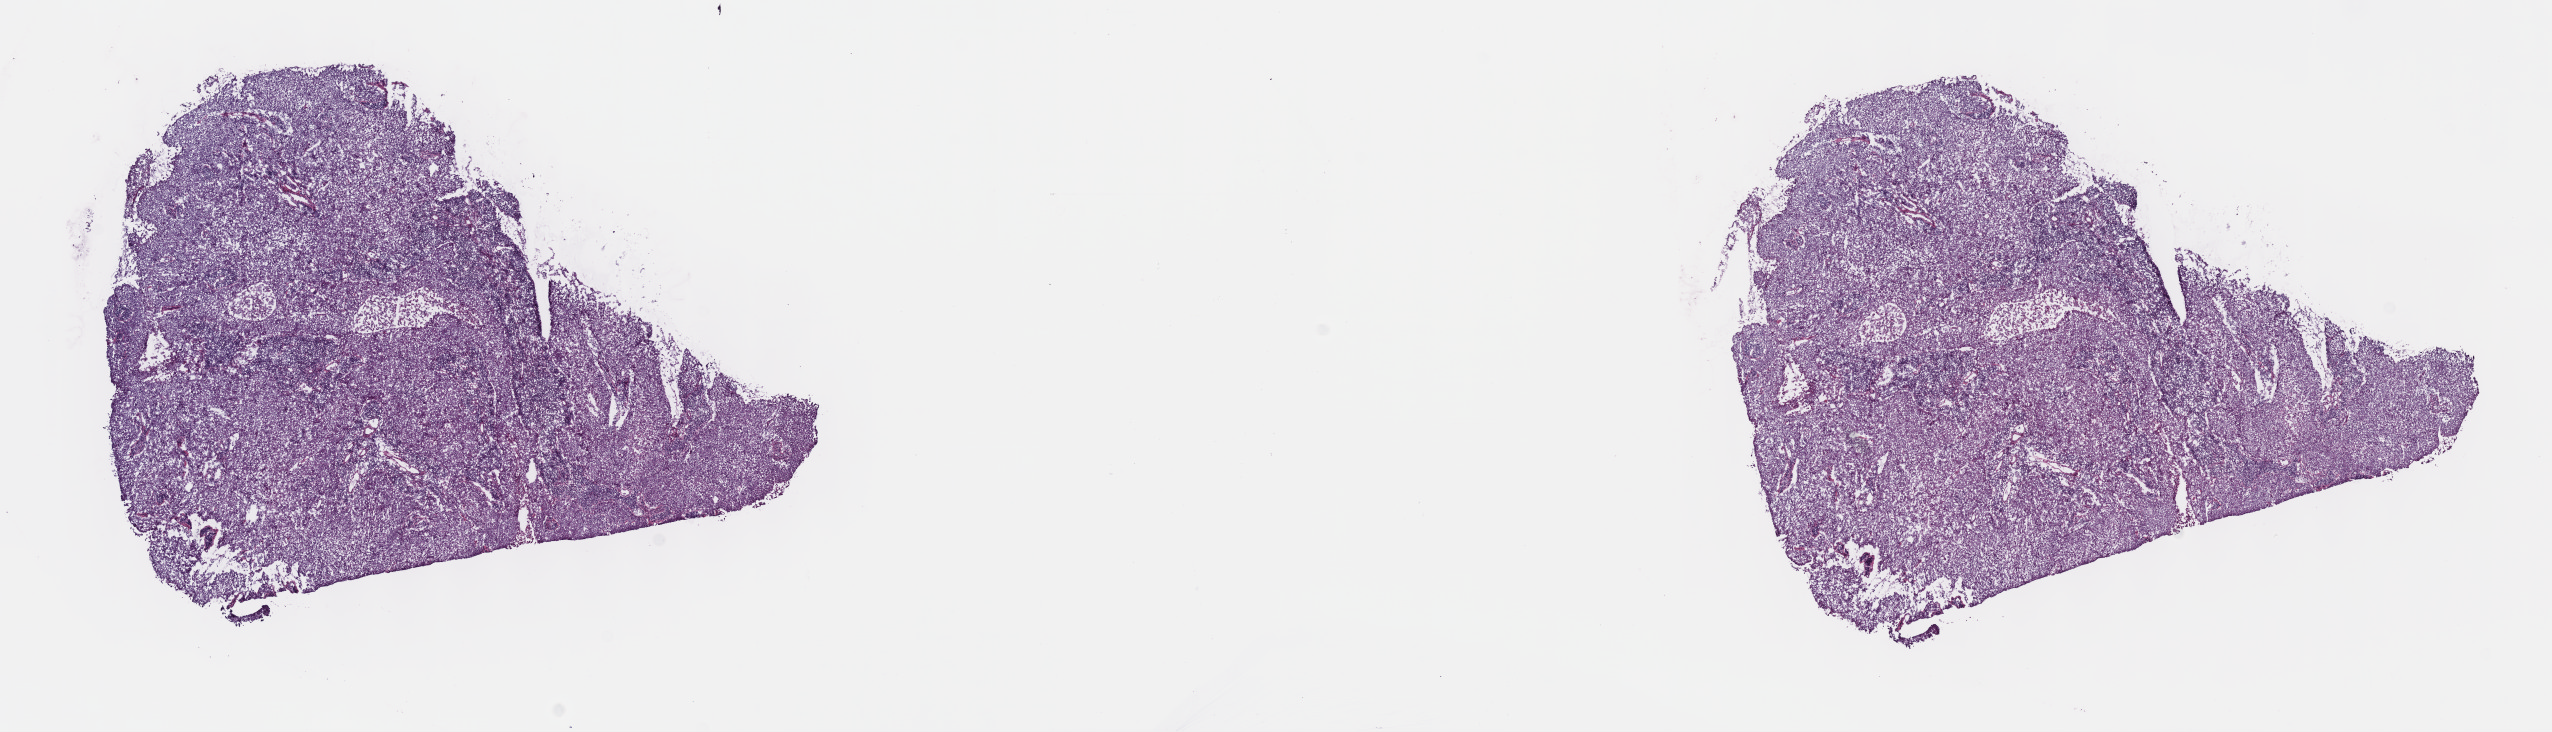
Digitized H&E tissue section (whole slide) — whole scanned area (about 20.6 x 5.9 mm) shown as a low-resolution overview, frozen section from the top of the tissue portion, sample: primary tumour, cervix. Female patient; age at initial diagnosis 51 years. Histologic grade: G2 (moderately differentiated). Pathologist review of this section (percent, as recorded): tumour cells 75%, tumour nuclei 75%, normal cells 0%, stromal cells 20%, necrosis 5%. Infiltration values recorded for this section: lymphocyte infiltration 40%, monocyte infiltration 20%, neutrophil infiltration 20%.
Diagnosis: Squamous cell carcinoma, NOS (cervix uteri). FIGO stage: IIB.